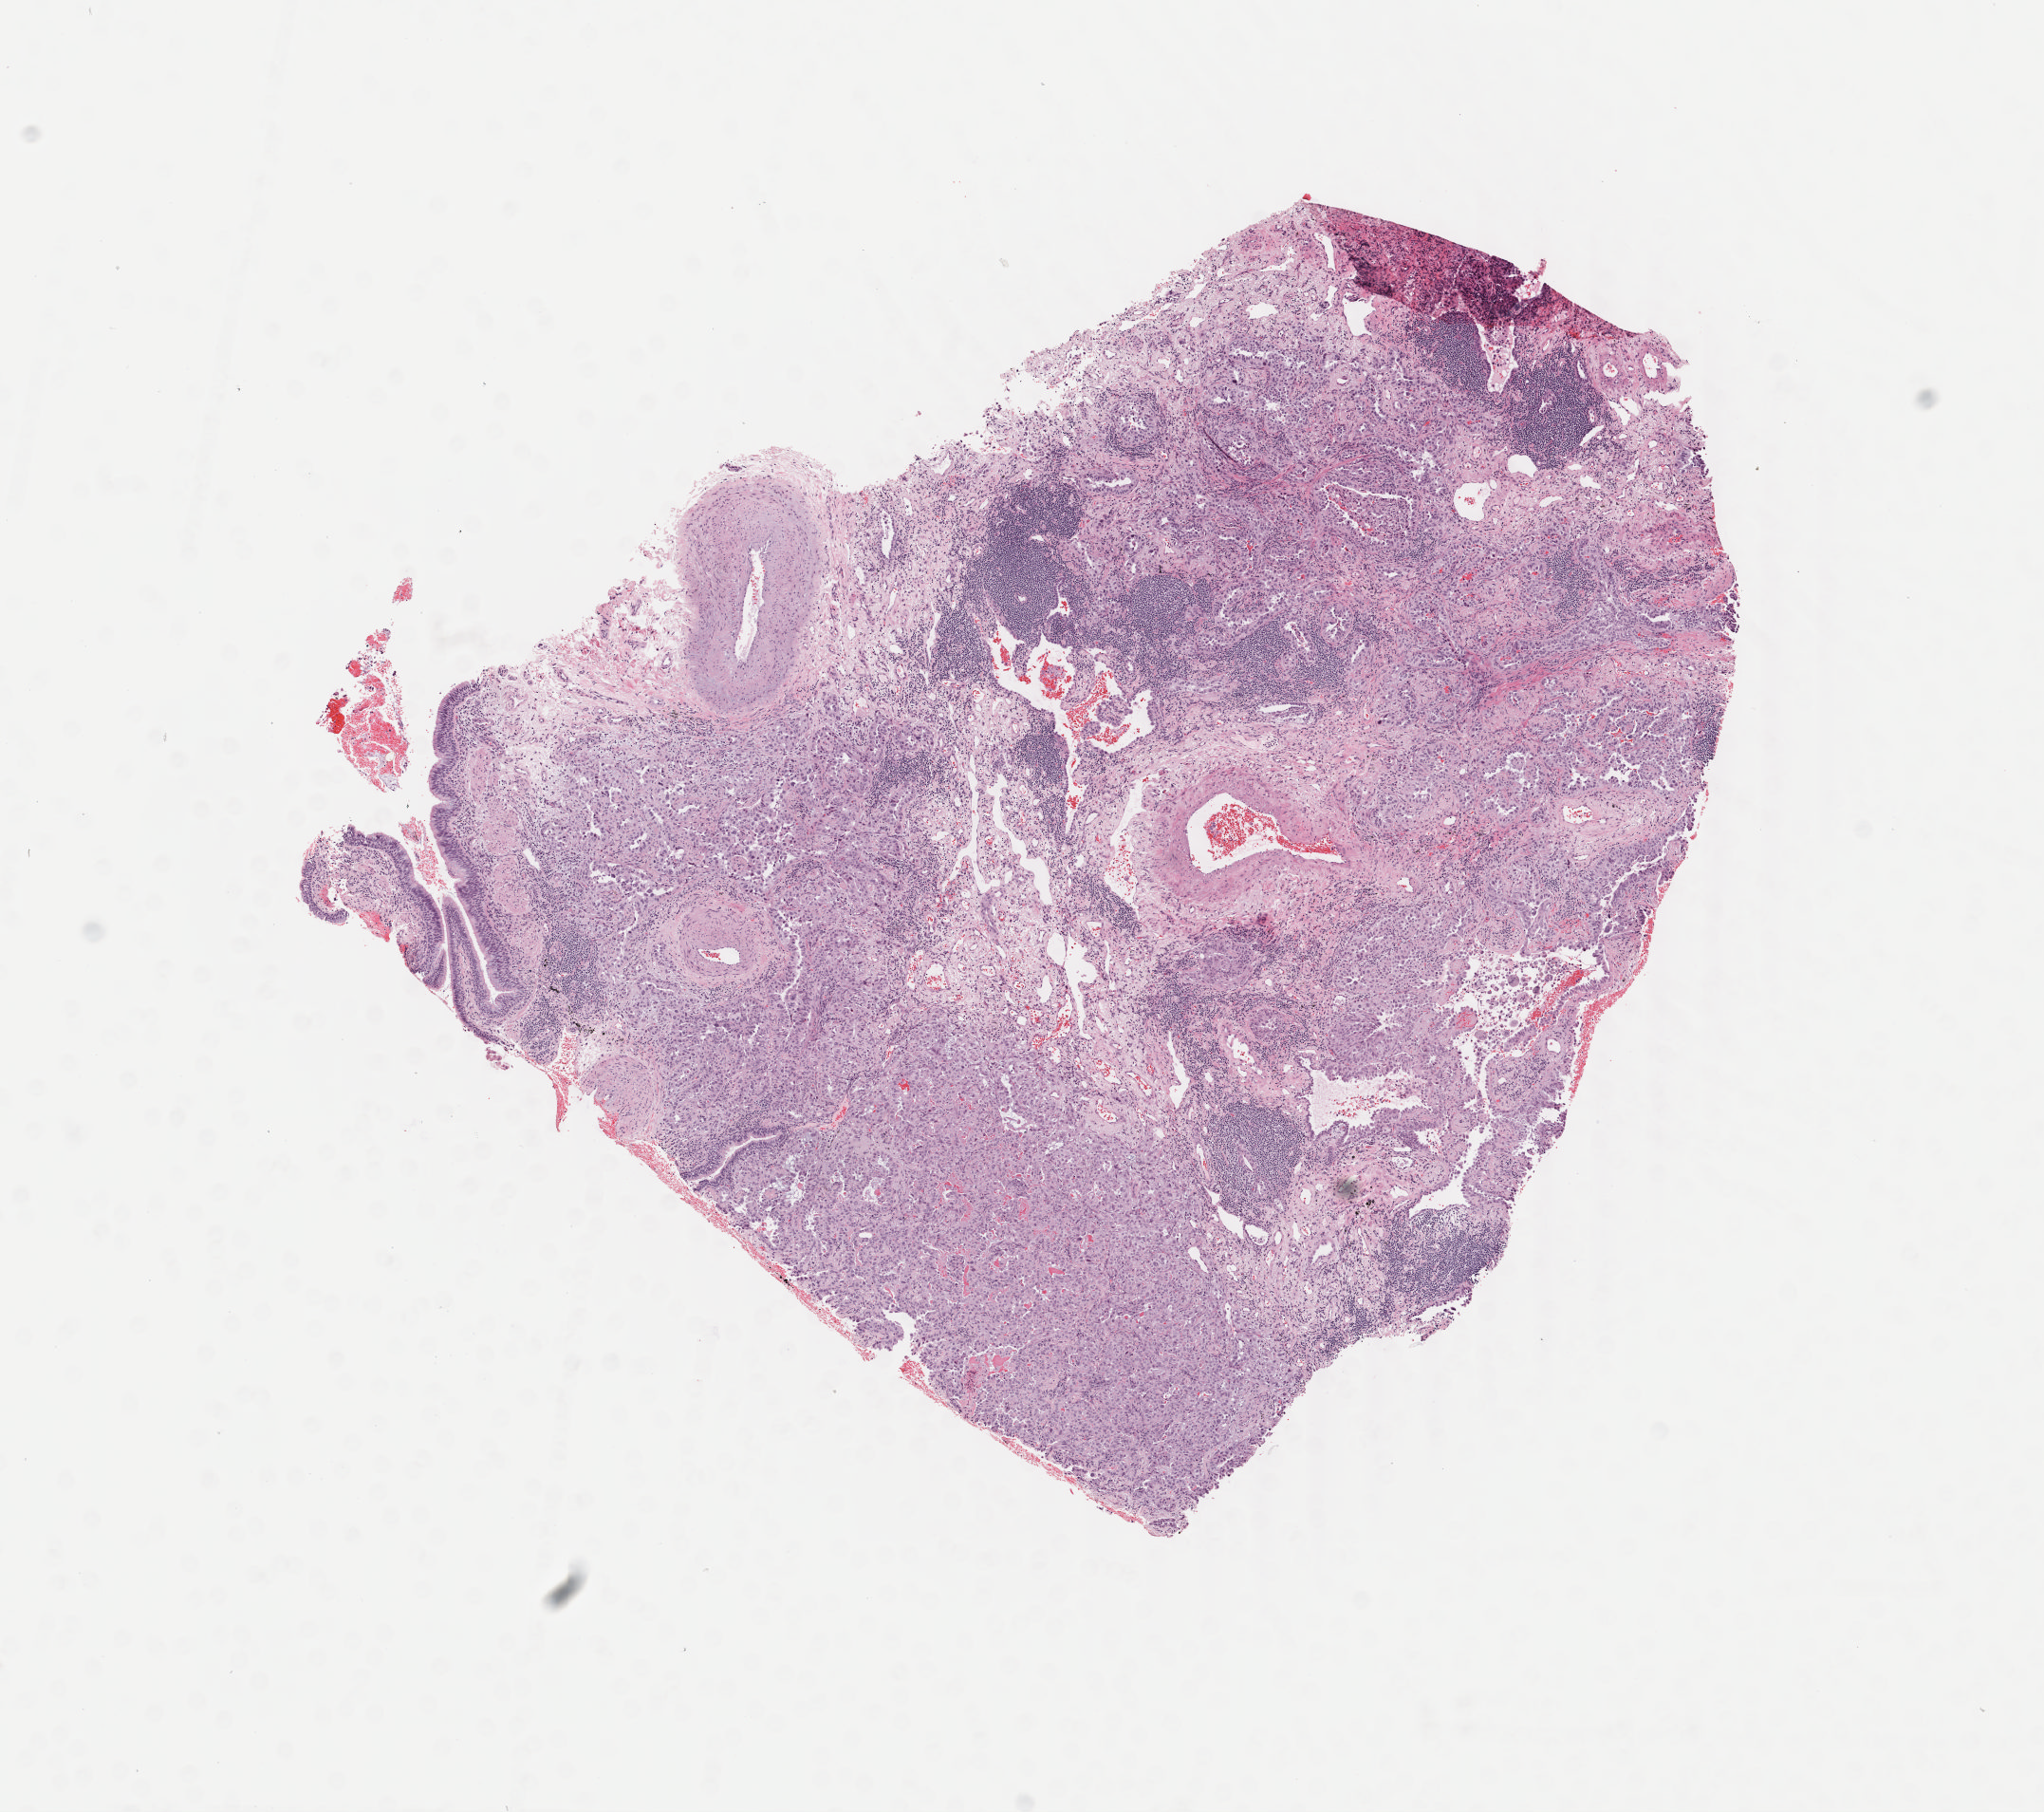
Digitized H&E-stained tissue section (whole slide), whole scanned area (about 8.6 x 7.6 mm) shown as a low-resolution overview. Frozen section. Primary tumour sample from the lung. Patient: female, age at initial diagnosis 67 years. Composition of this section per pathologist review: tumour cells 55%, tumour nuclei 65%, normal cells 3%, stromal cells 42%, necrosis 0%. Infiltration values recorded for this section: lymphocyte infiltration 20%, monocyte infiltration 3%, neutrophil infiltration 3%.
AJCC pathologic stage: IA (7th edition). Diagnosis: Adenocarcinoma, NOS (upper lobe, lung).